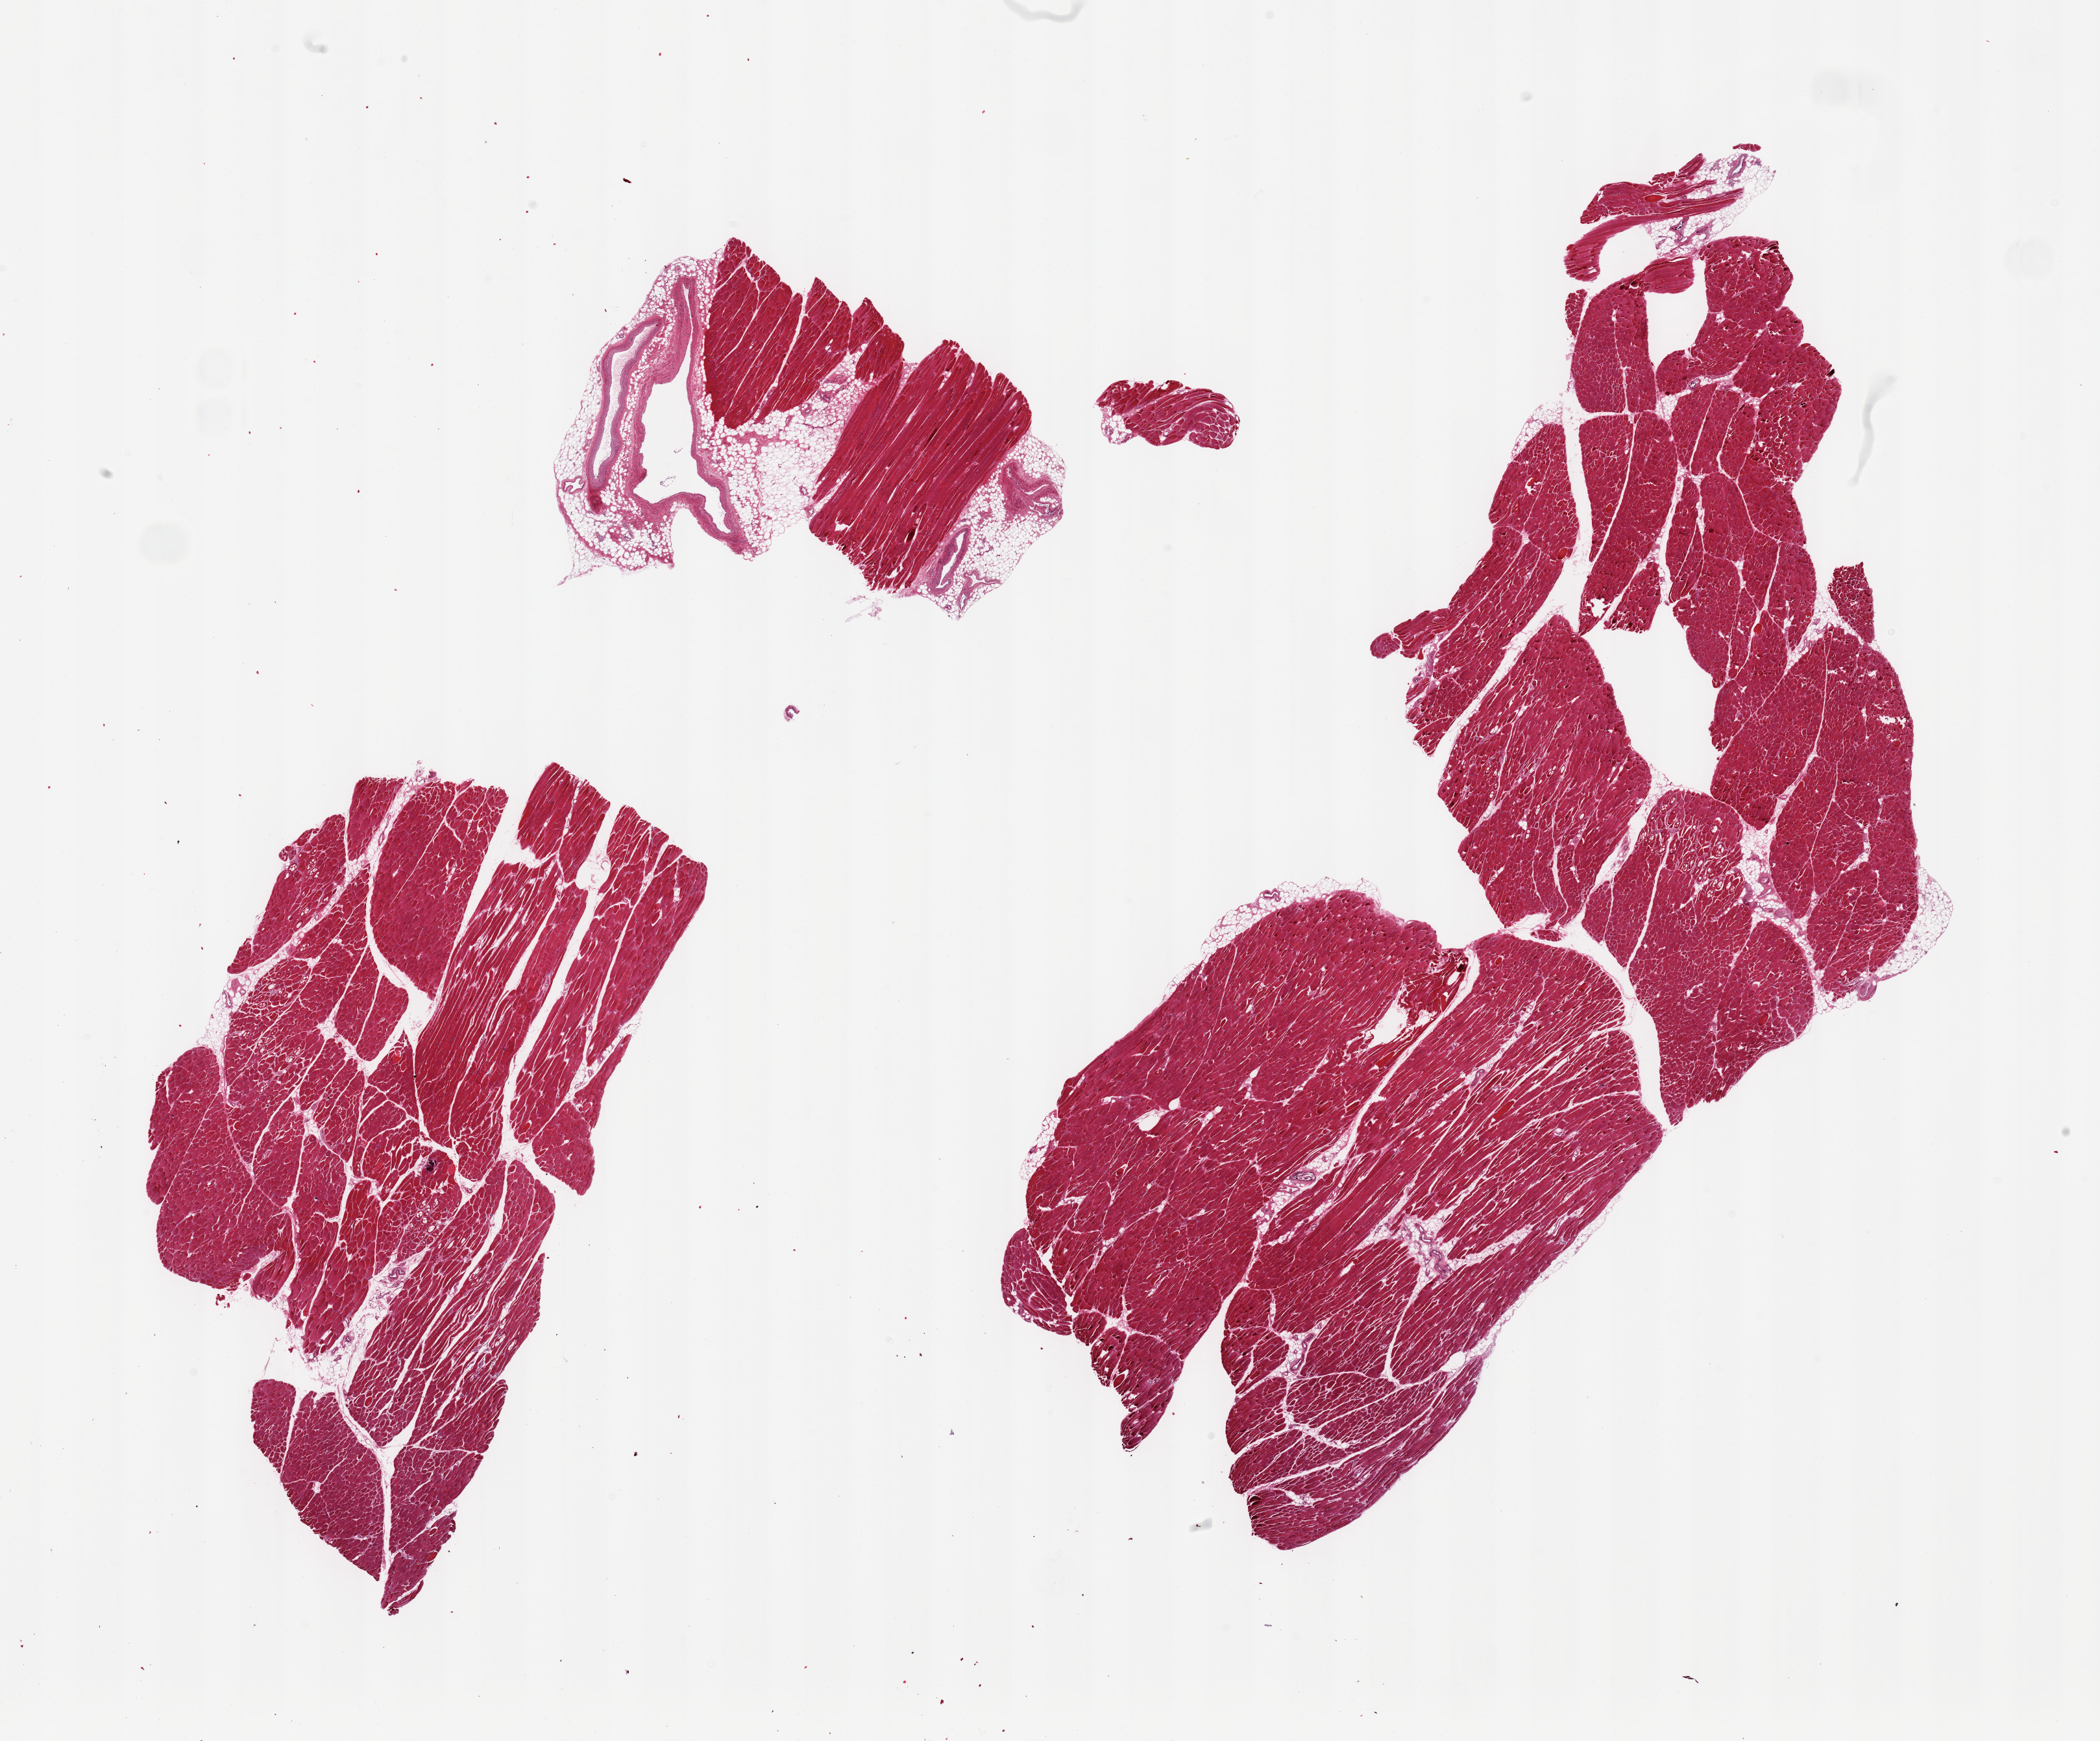
Digitized haematoxylin and eosin-stained section, brightfield, whole scanned area (about 25.6 x 21.2 mm, slide scanned at 20x) shown as a low-resolution overview, PAXgene-fixed paraffin-embedded (PFPE) section, section of skeletal muscle (target tissue), donor tissue sample. Donor: female.
Pathologist's review note for this sample: 2 pieces, ~5-10% interstitial fat/vascular elements.